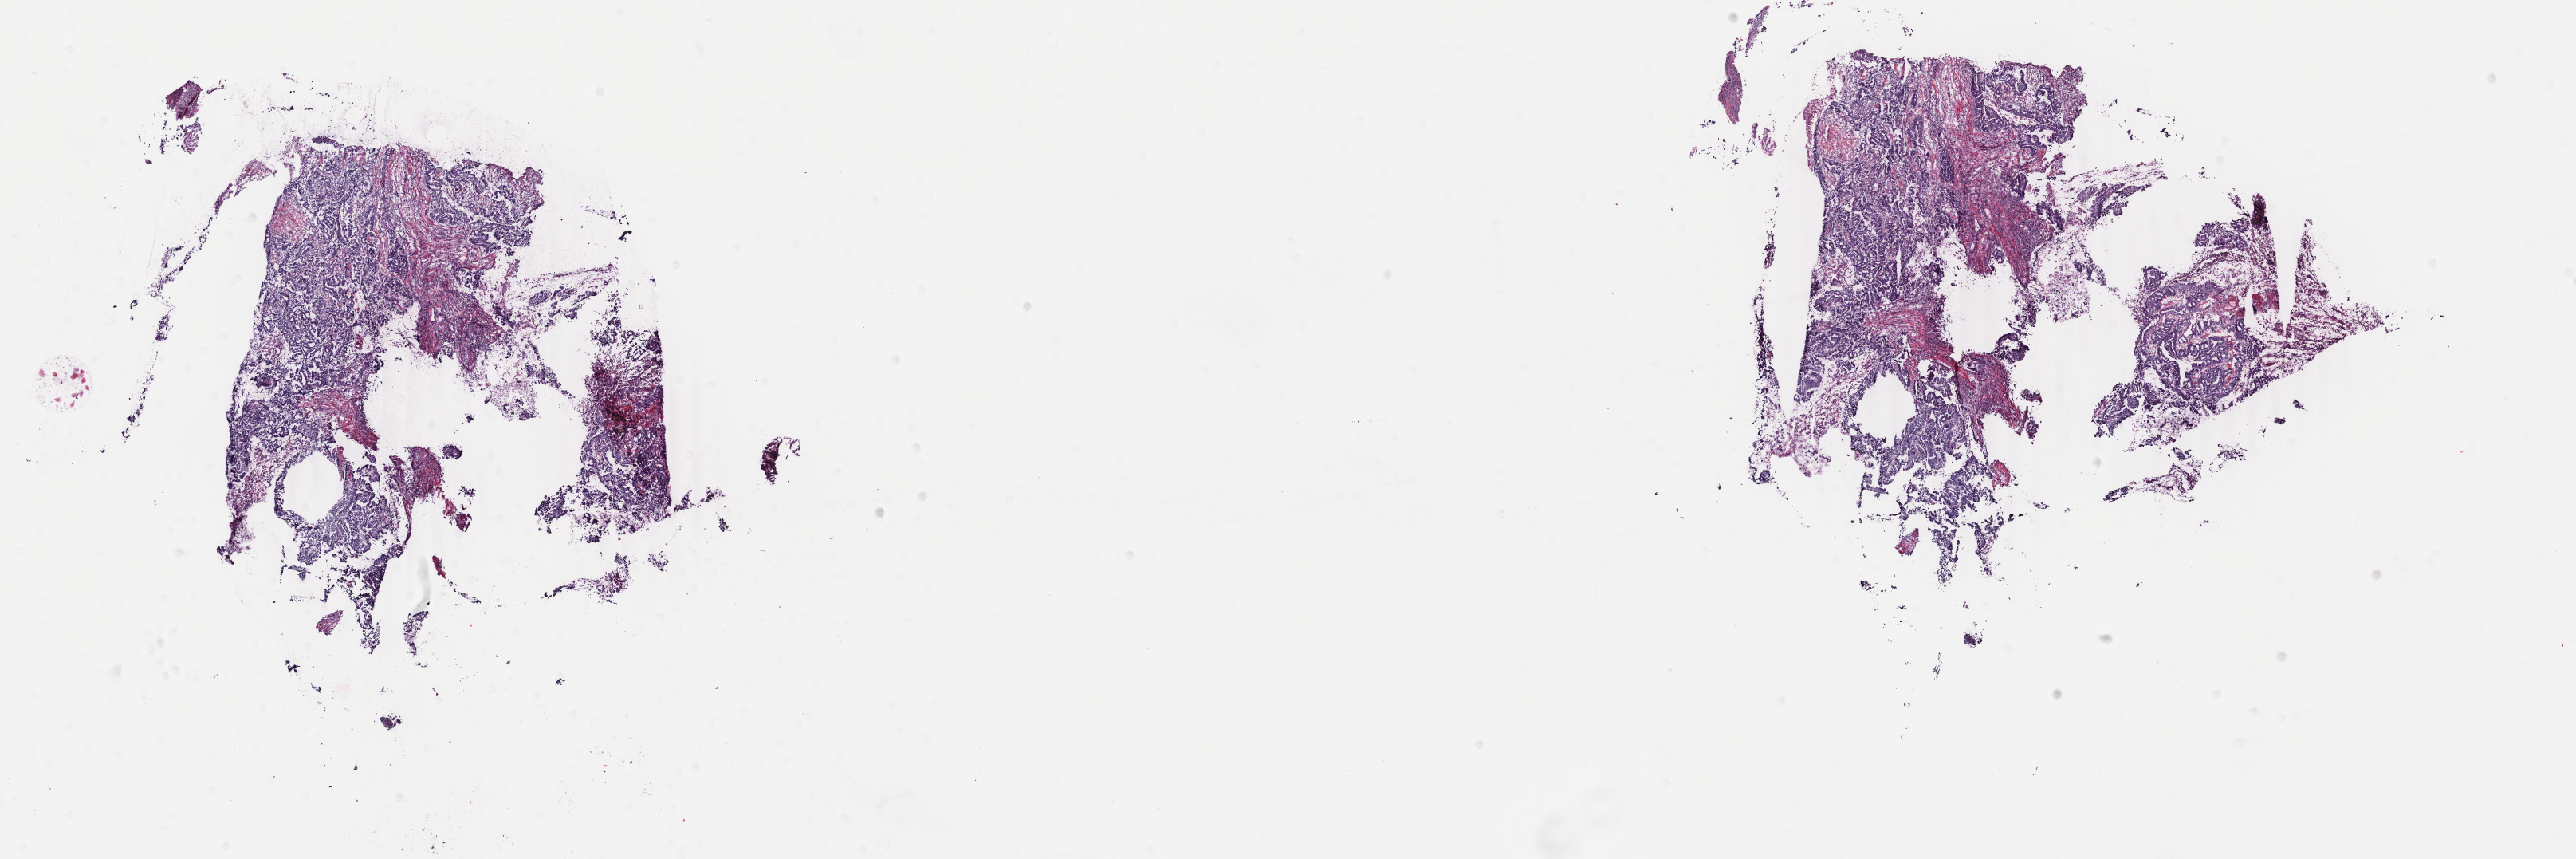
Hematoxylin and eosin (H&E) stained whole-slide image, a low-resolution overview of the entire scanned area, about 25.7 x 8.6 mm (from a 40x scan). Frozen section. Uterus, primary tumour sample. Female patient; age at initial diagnosis 88 years. Composition of this section per pathologist review: tumour cells 70%, tumour nuclei 80%.
Histologic diagnosis: Endometrioid adenocarcinoma, NOS (endometrium).